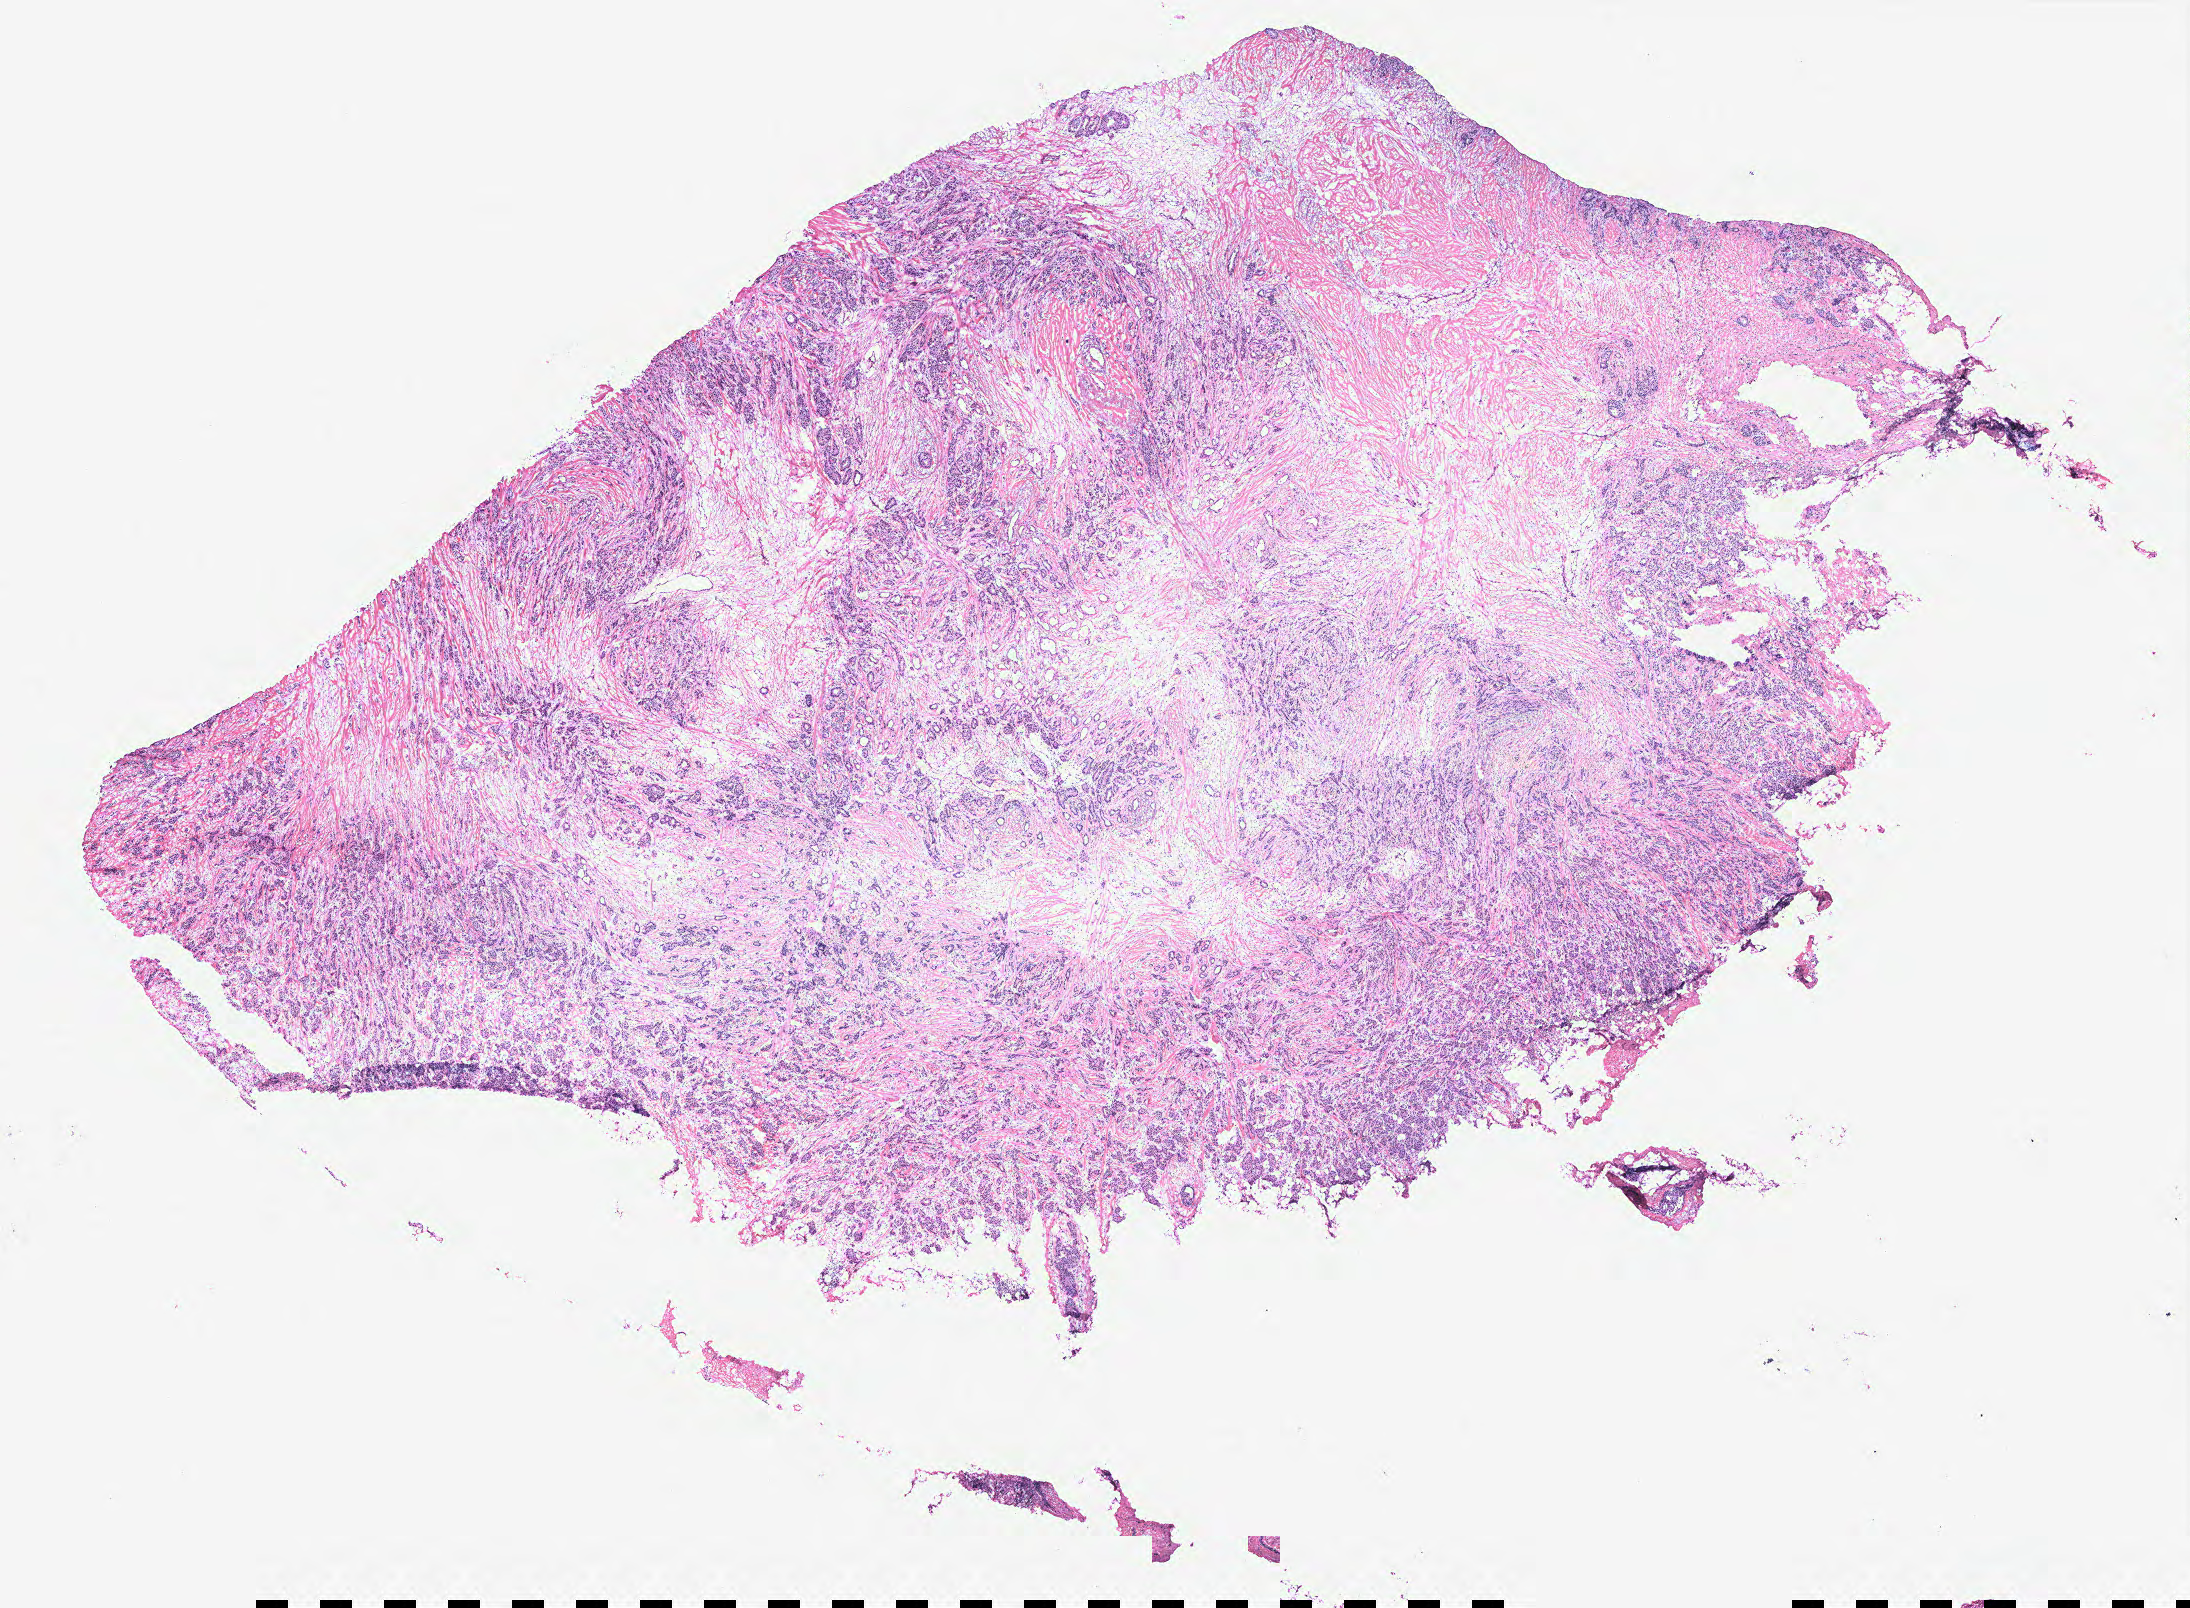
Whole-slide histology image, H&E — low-resolution overview of the scanned area, about 17.5 x 12.9 mm, breast, tumour tissue. Patient: female, age 73 years.
AJCC pathologic stage: IA. Diagnosis: Infiltrating duct carcinoma, NOS.